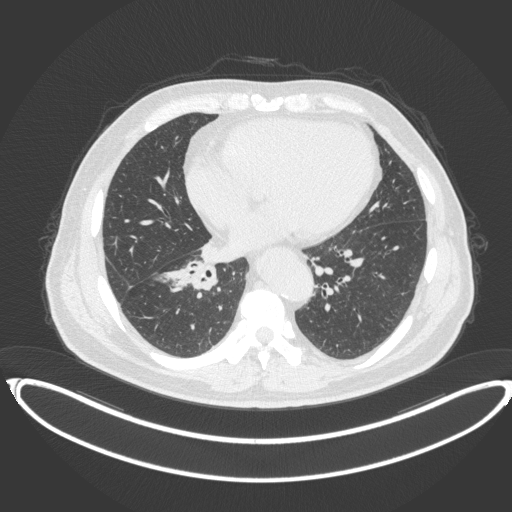
Chest CT, one axial slice; position 164 of 383 along the scan axis; lung window (W 1500 / L -600 HU); 1 mm slice thickness; 512 × 512 image matrix. Patient: male, 61 years. From the clinical record (not read from this slice): clinical TNM (as recorded): T1b N1 M0.
Structures marked on this image (rectangle marked by the reading radiologist):
- lung tumour (recorded histology: squamous cell carcinoma): bounding box [x1, y1, x2, y2] px = [180, 258, 221, 294]